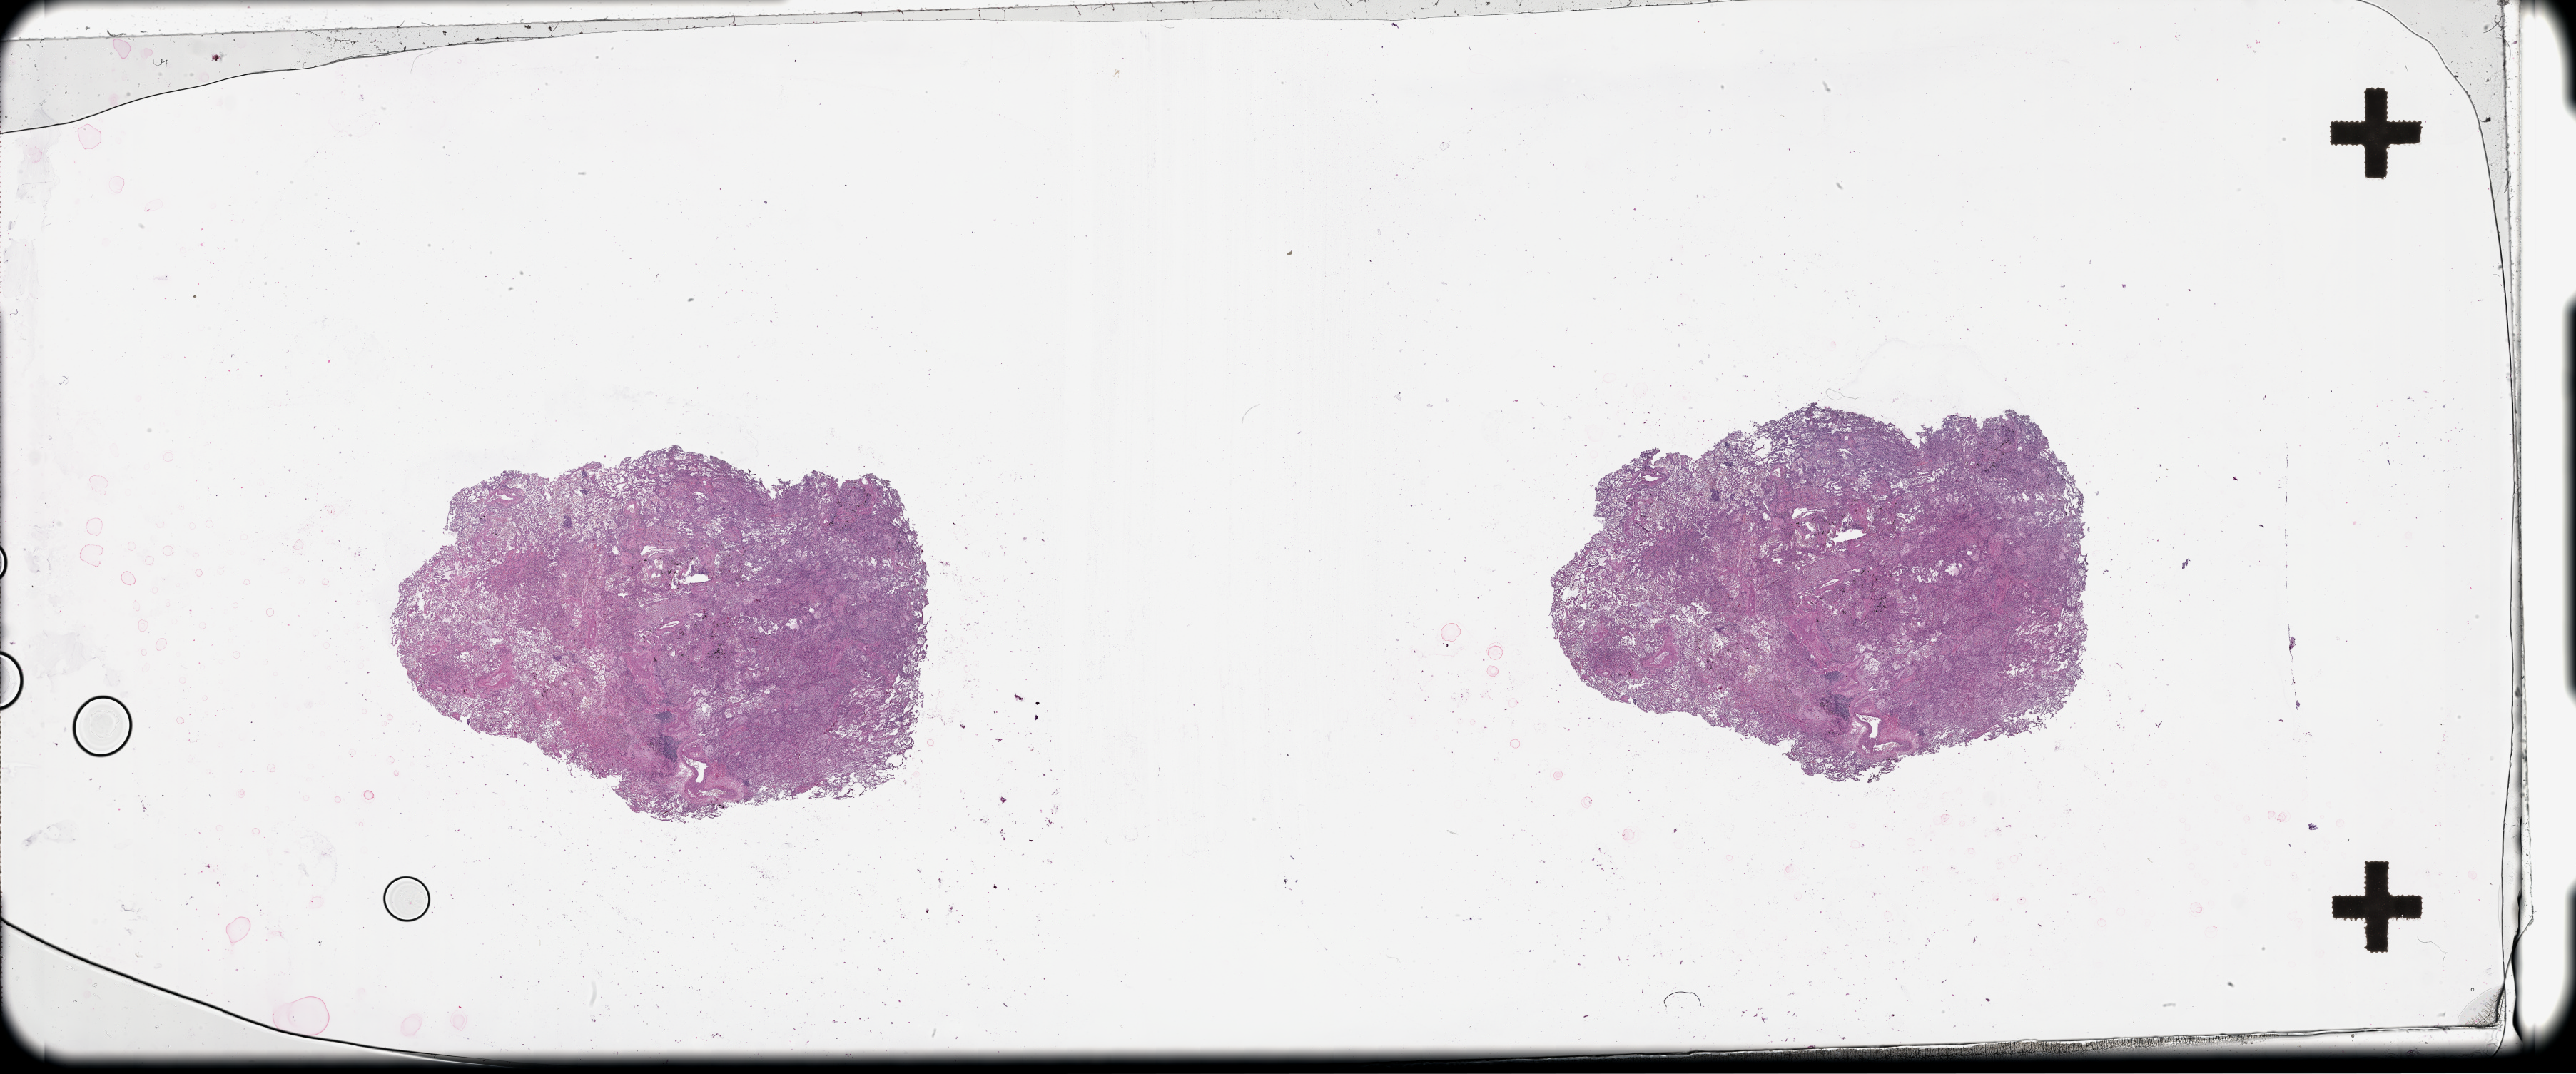
Digitized Hematoxylin and eosin (H&E) stained tissue section (whole slide) — low-resolution overview of the scanned area, about 58.1 x 24.2 mm, lung, tumour tissue. 58-year-old female patient.
Patient diagnosis (cohort enrolment): squamous cell carcinoma (lung).